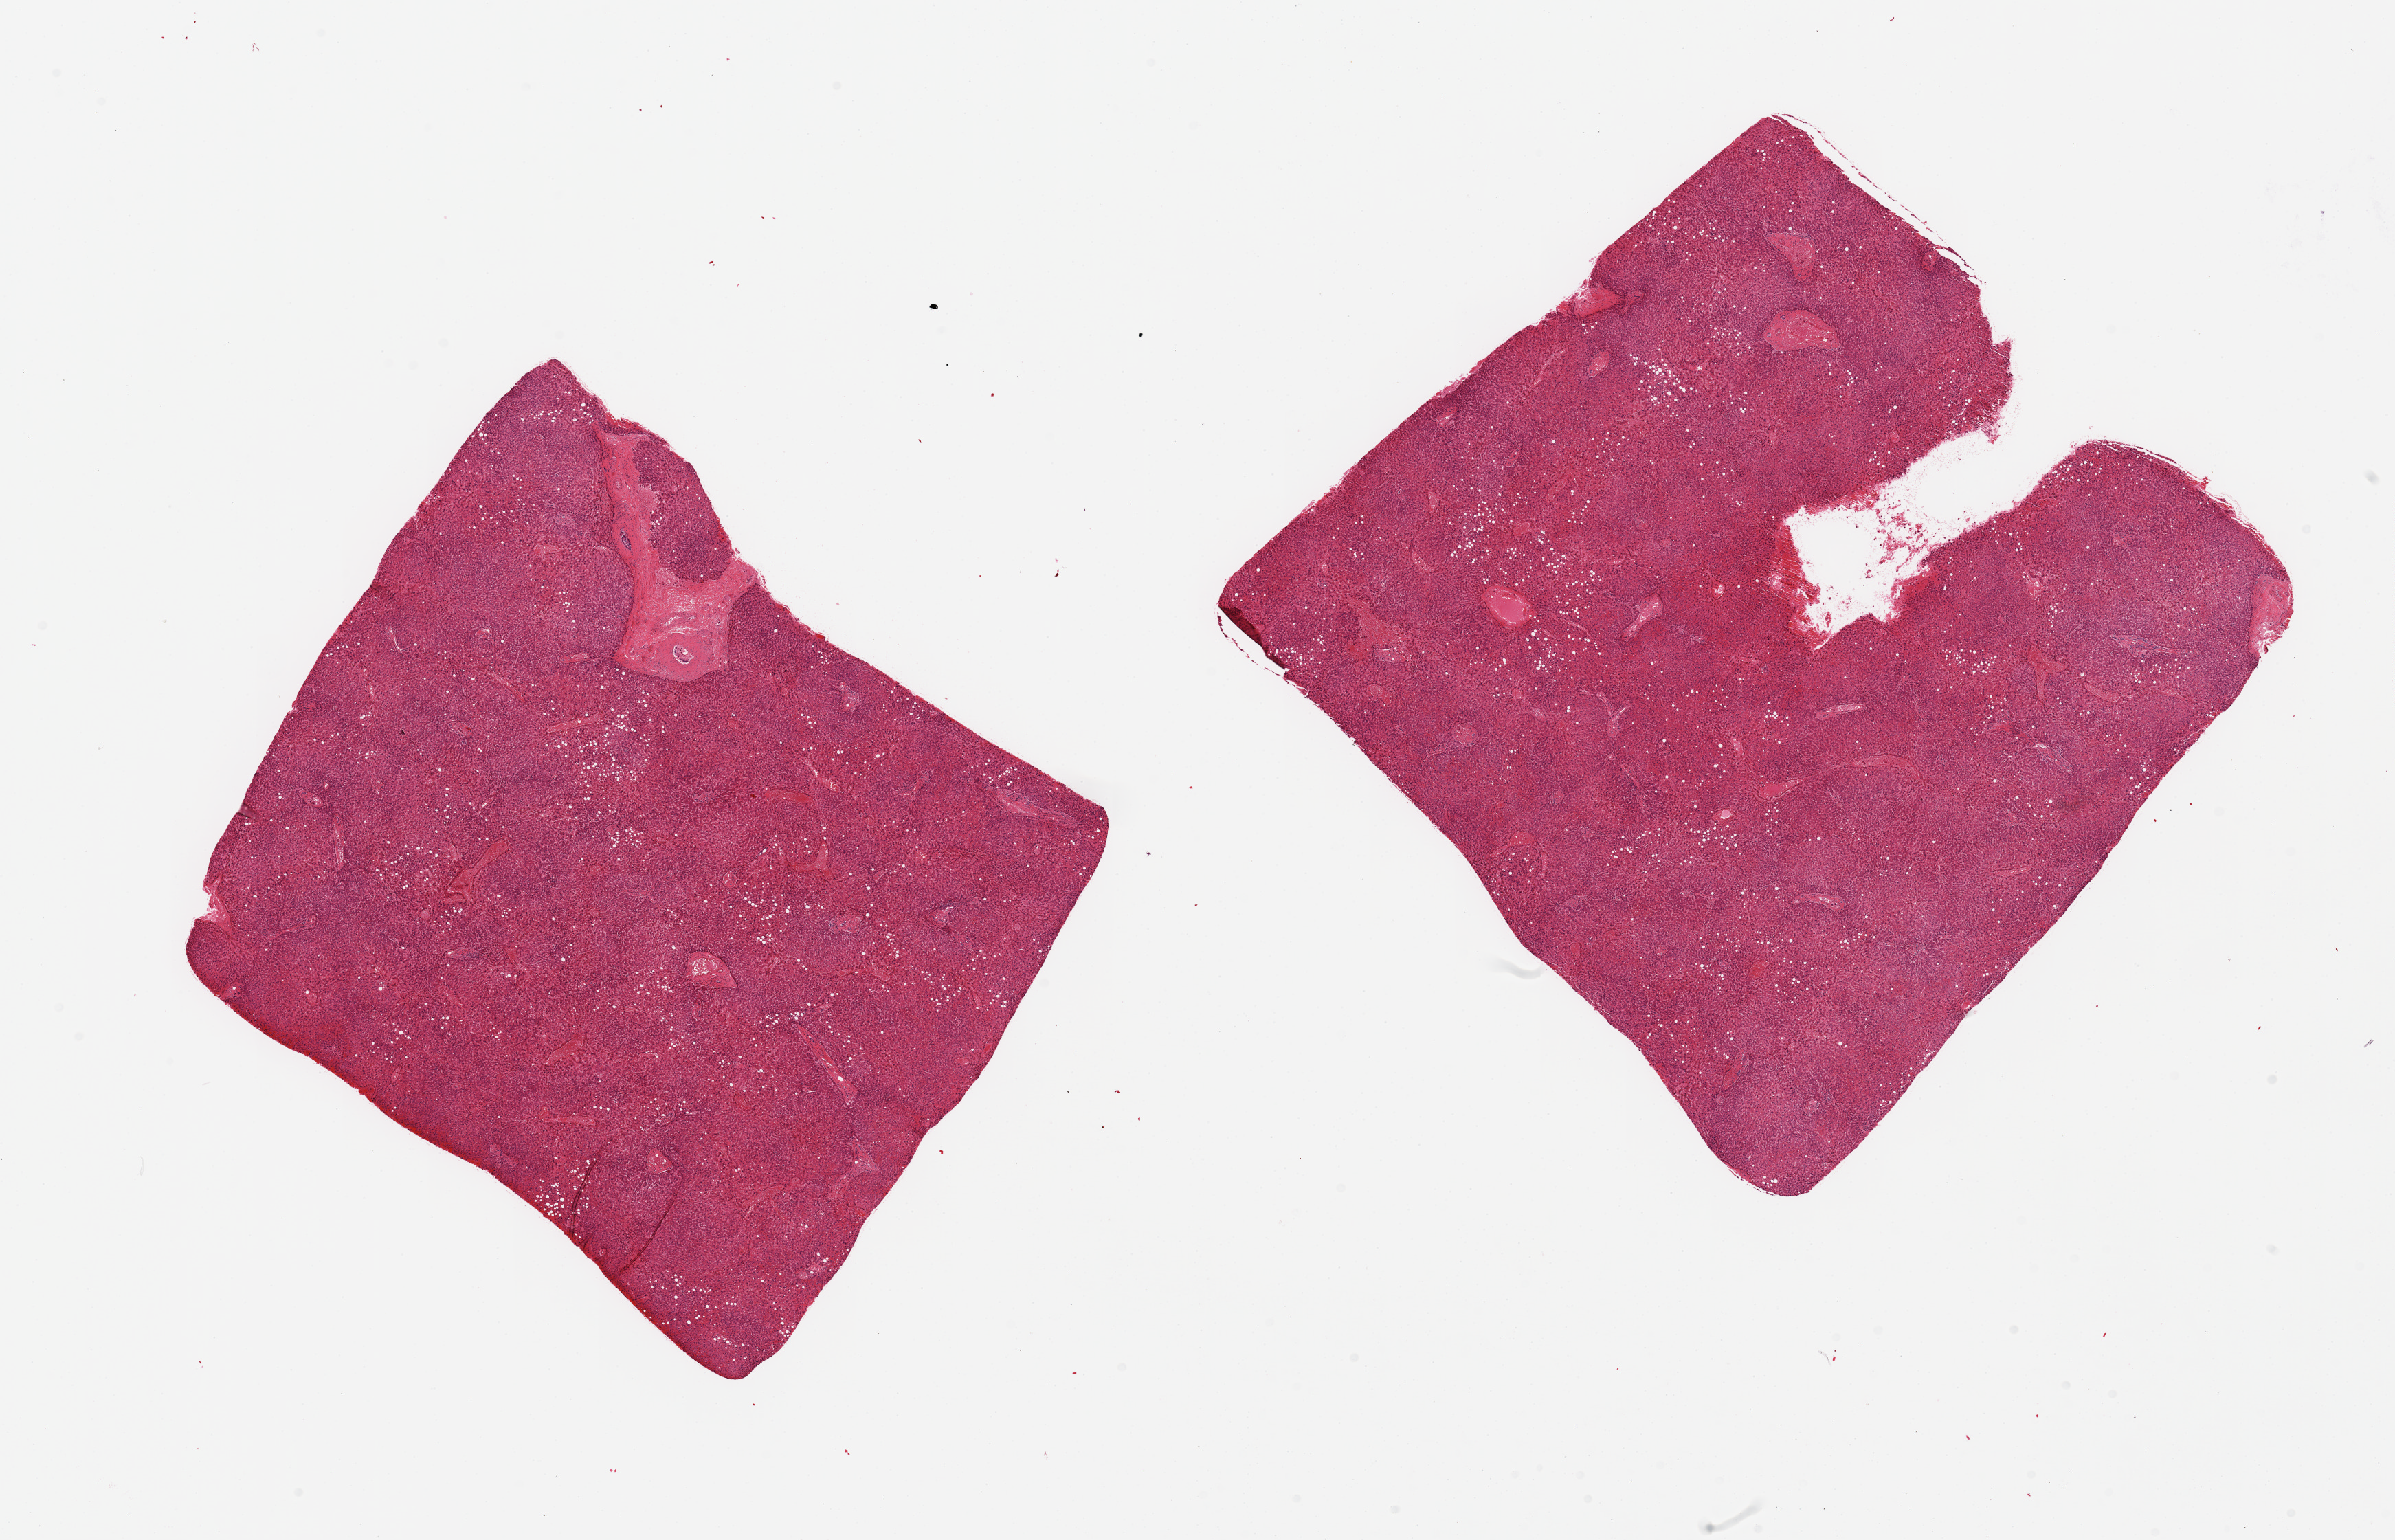
Whole-slide image, haematoxylin and eosin stain — low-resolution overview of the scanned area, about 27.6 x 17.7 mm (acquisition: 20x scan), PAXgene-fixed paraffin-embedded (PFPE) section, sampled site (target tissue): liver, donor tissue sample. Donor sex: male.
Reviewer comment on this tissue sample: 2 pieces; moderate central congestion; 5% macrovesicular steatosis.